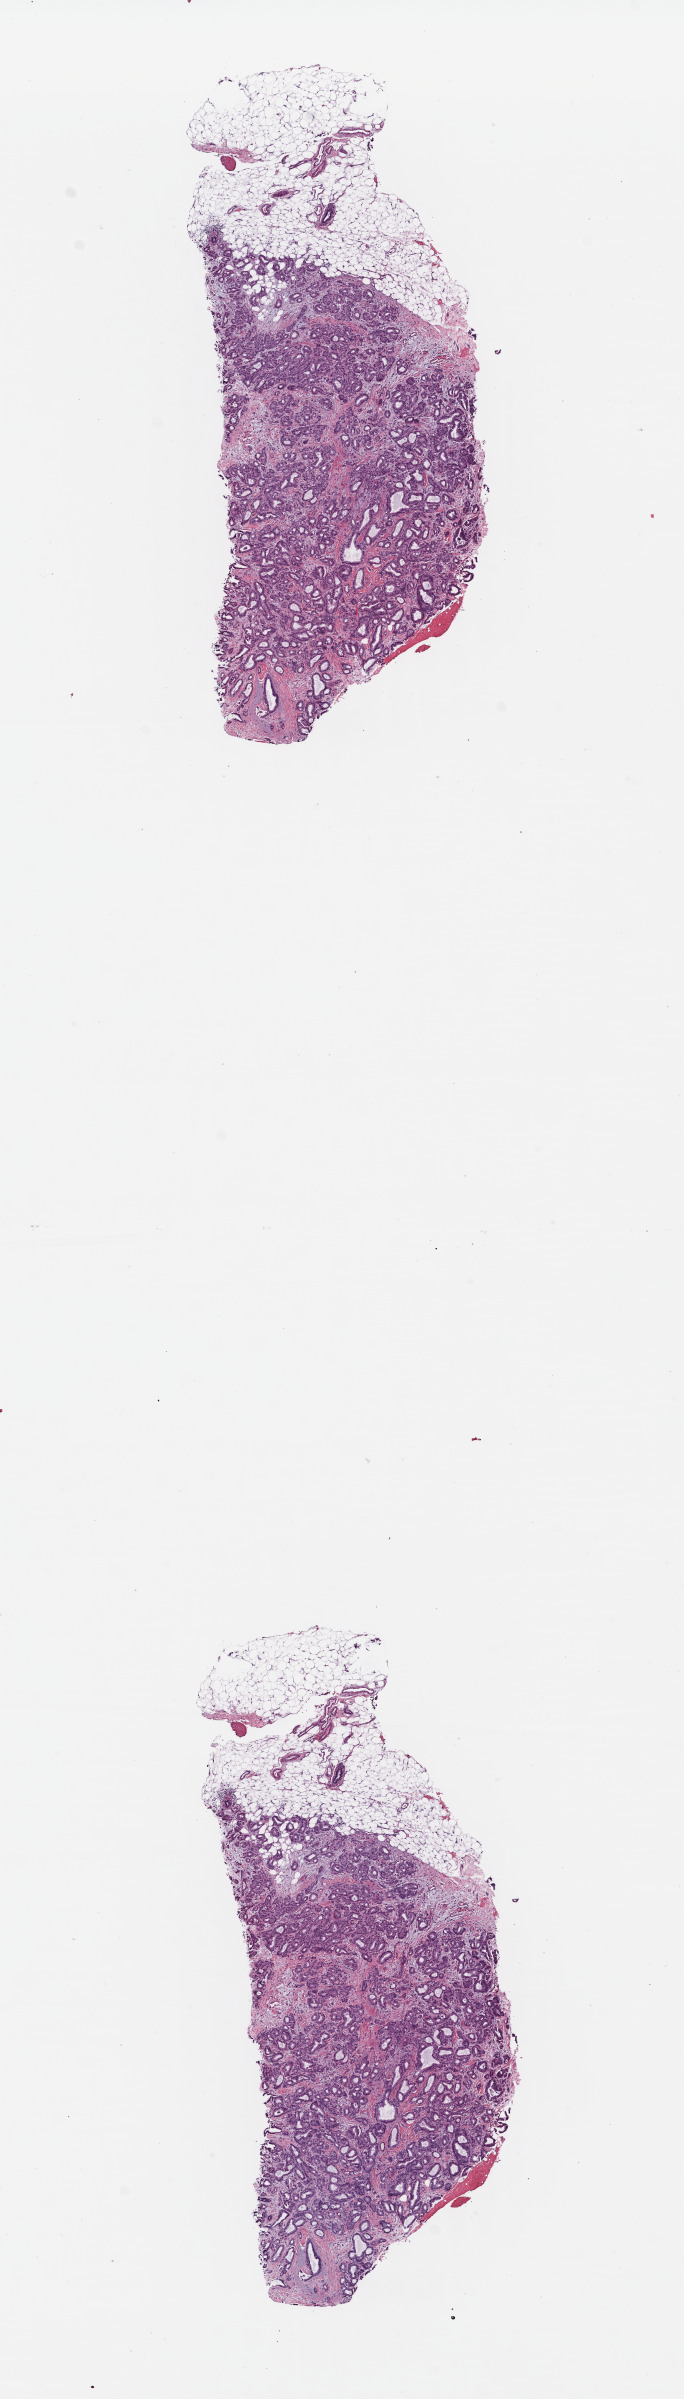
Whole-slide histology image, Hematoxylin and eosin (H&E) stained, a low-resolution overview of the entire scanned area, about 5.4 x 18.9 mm. Formalin-fixed paraffin-embedded (FFPE) diagnostic section. Primary tumour sample from the breast. Female, age 79 years at initial diagnosis.
Diagnosis: Infiltrating duct carcinoma, NOS.